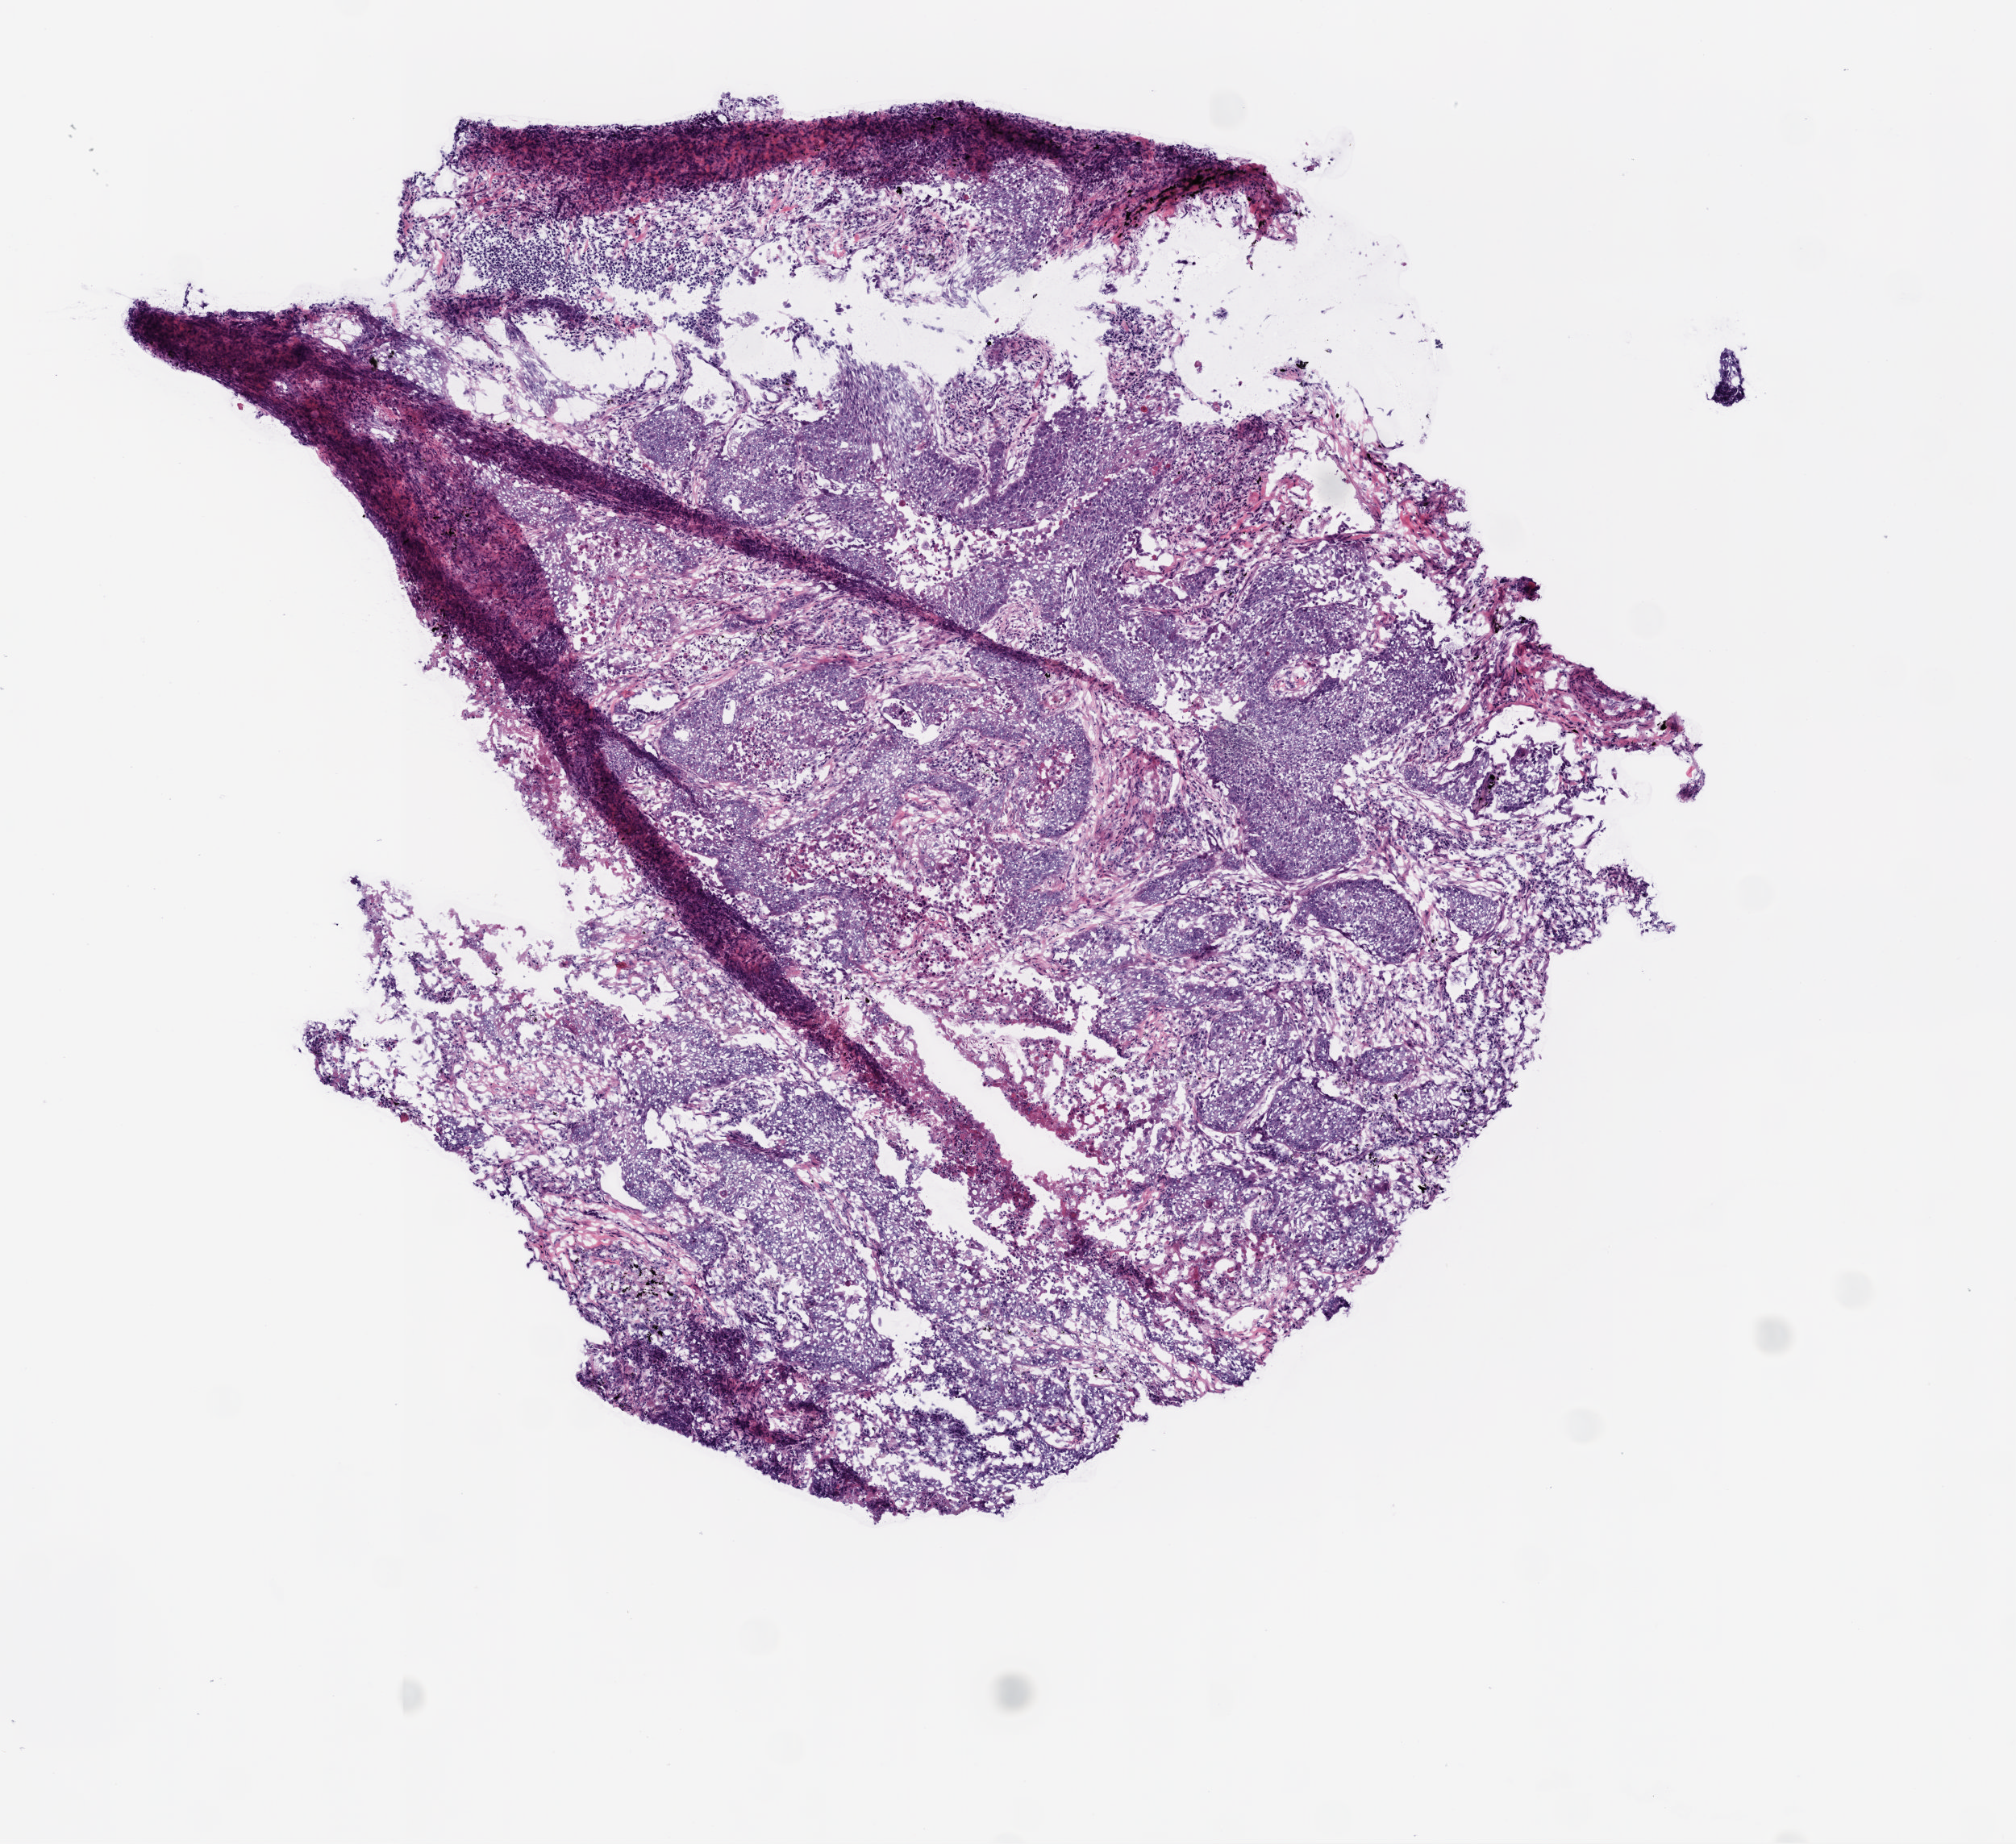
H&E-stained whole-slide image — shown as a low-resolution overview of the whole scanned area (about 5.0 x 4.6 mm, acquisition: 20x scan); frozen section from the top of the tissue portion; lung, primary tumour sample. Male patient; age at initial diagnosis 72 years. Composition of this section per pathologist review: tumour cells 75%, tumour nuclei 80%, normal cells 0%, stromal cells 15%, necrosis 10%. Infiltration values recorded for this section: lymphocyte infiltration 10%.
* AJCC pathologic stage: IB
* pathologic diagnosis: Squamous cell carcinoma, NOS (upper lobe, lung)